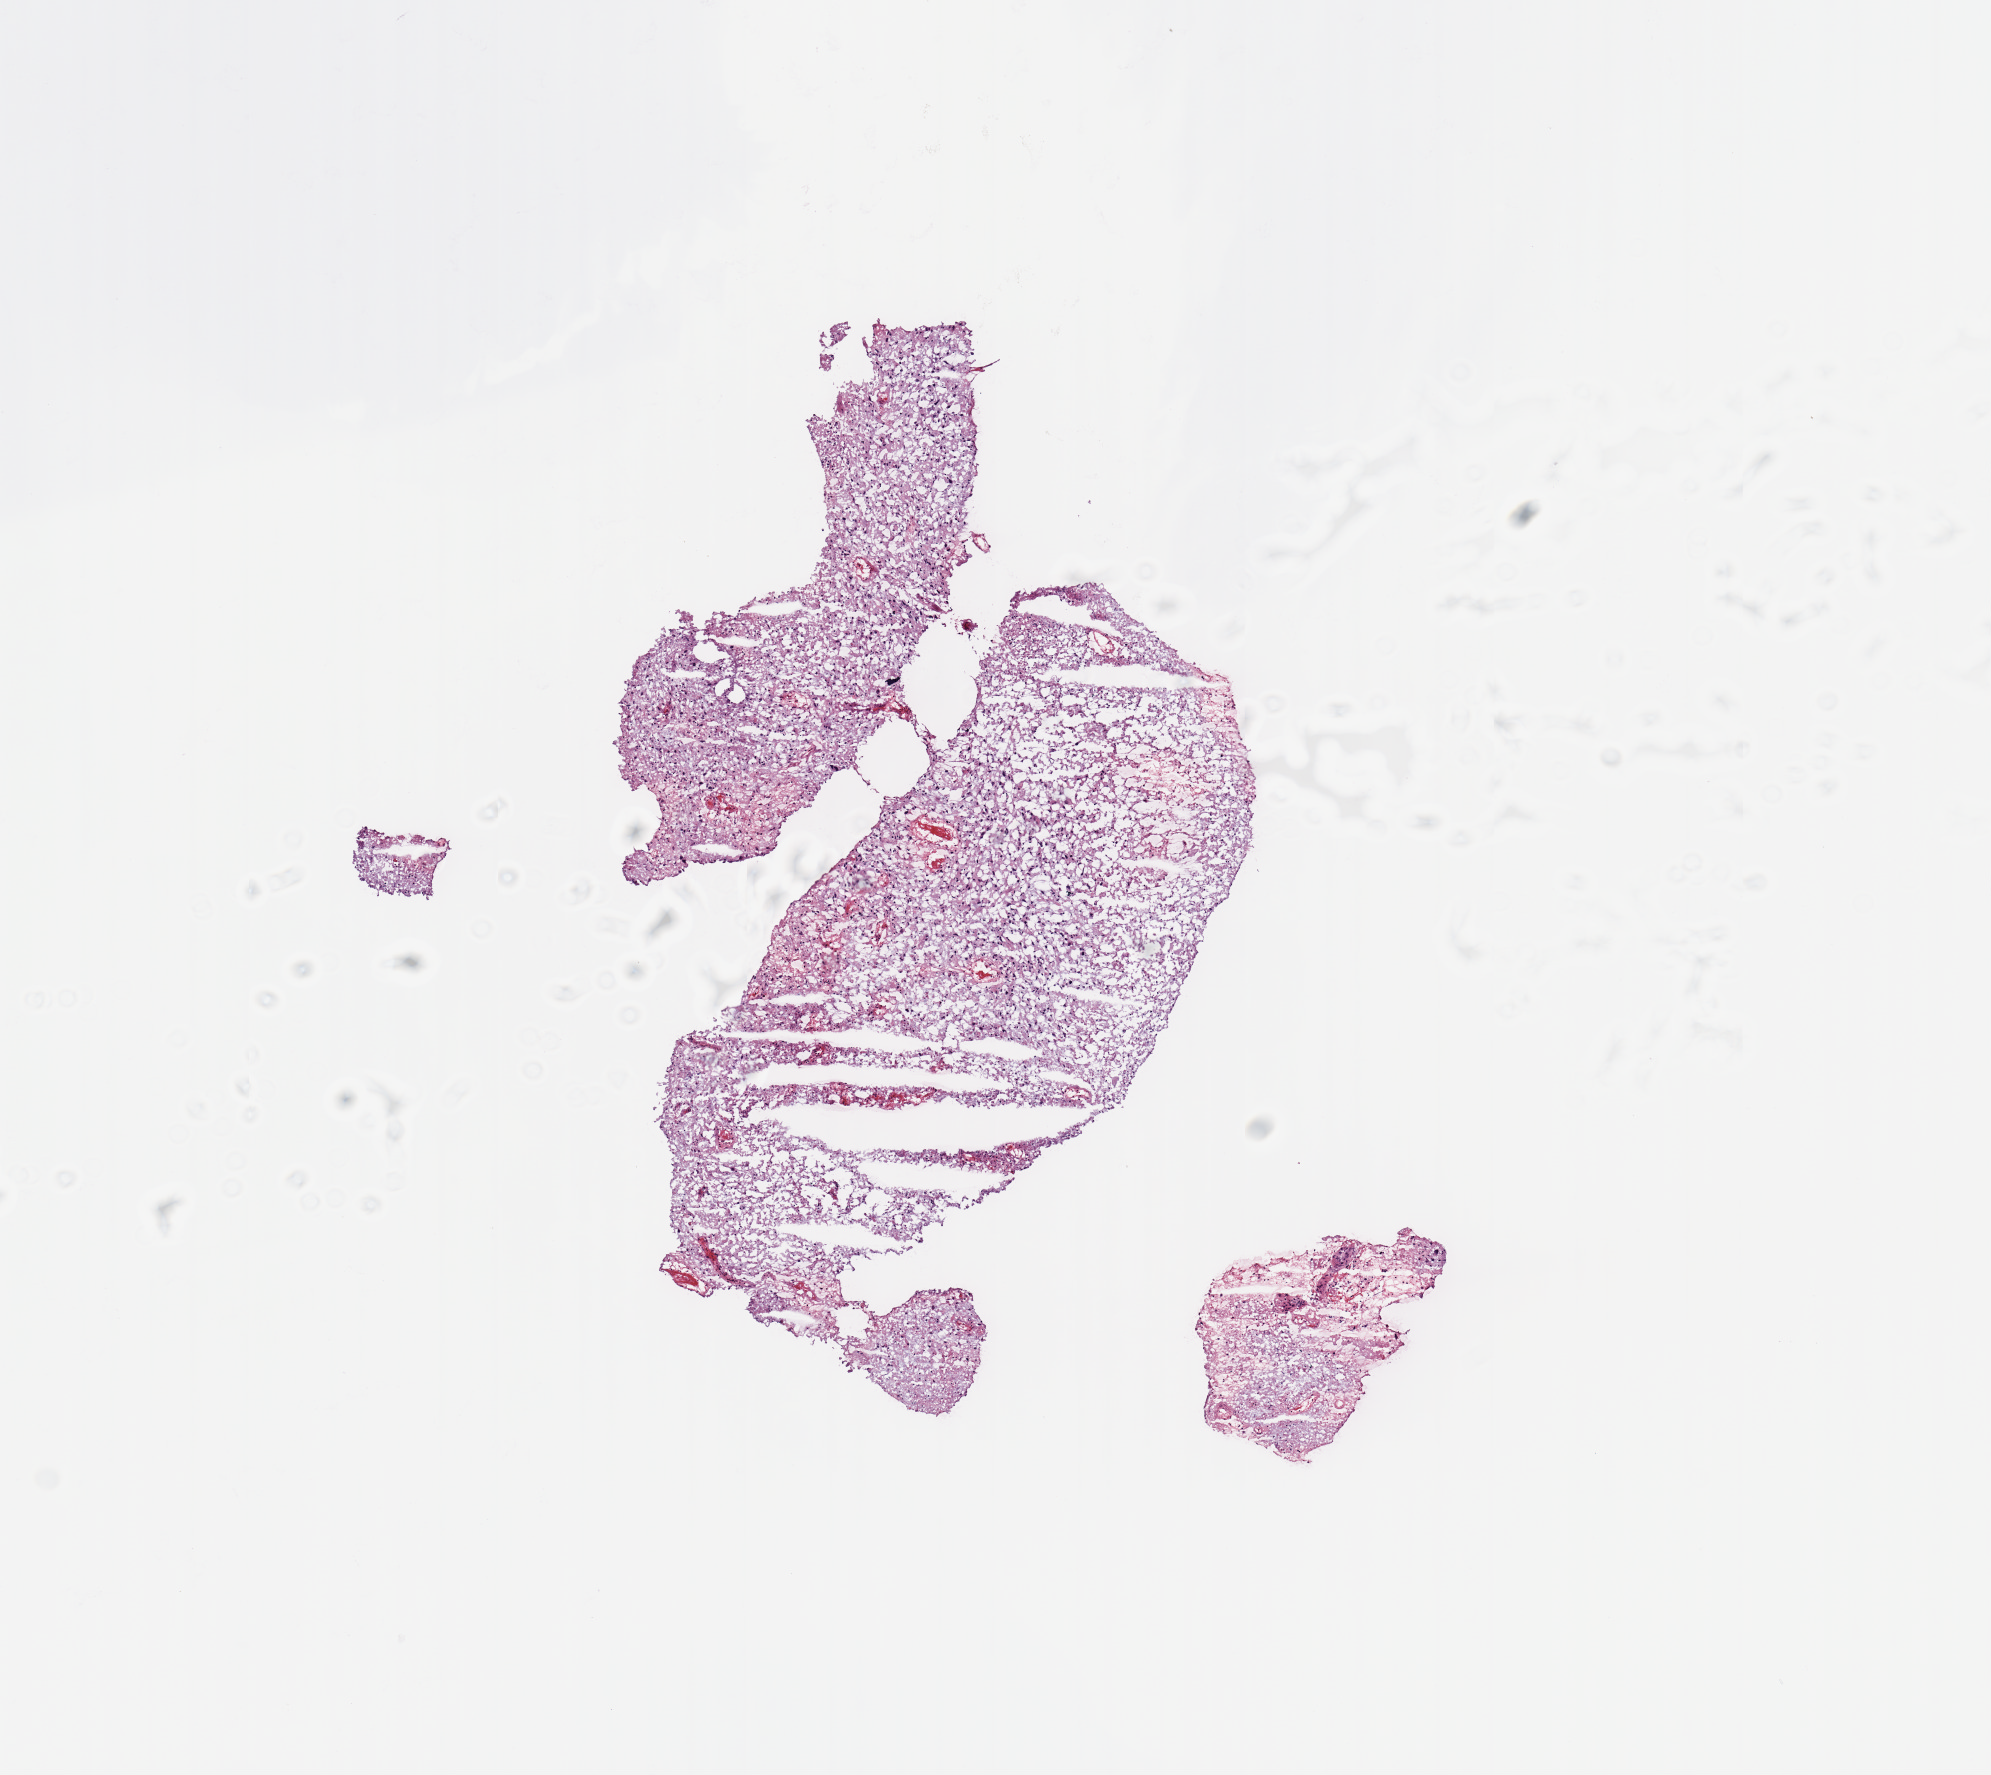
Whole-slide histology image, Hematoxylin and eosin (H&E) stained — low-resolution overview of the scanned area, about 7.9 x 7.0 mm (acquisition: 20x scan). Tumour tissue sample, brain. 57-year-old female patient.
Patient diagnosis (cohort enrolment): glioblastoma multiforme (brain).